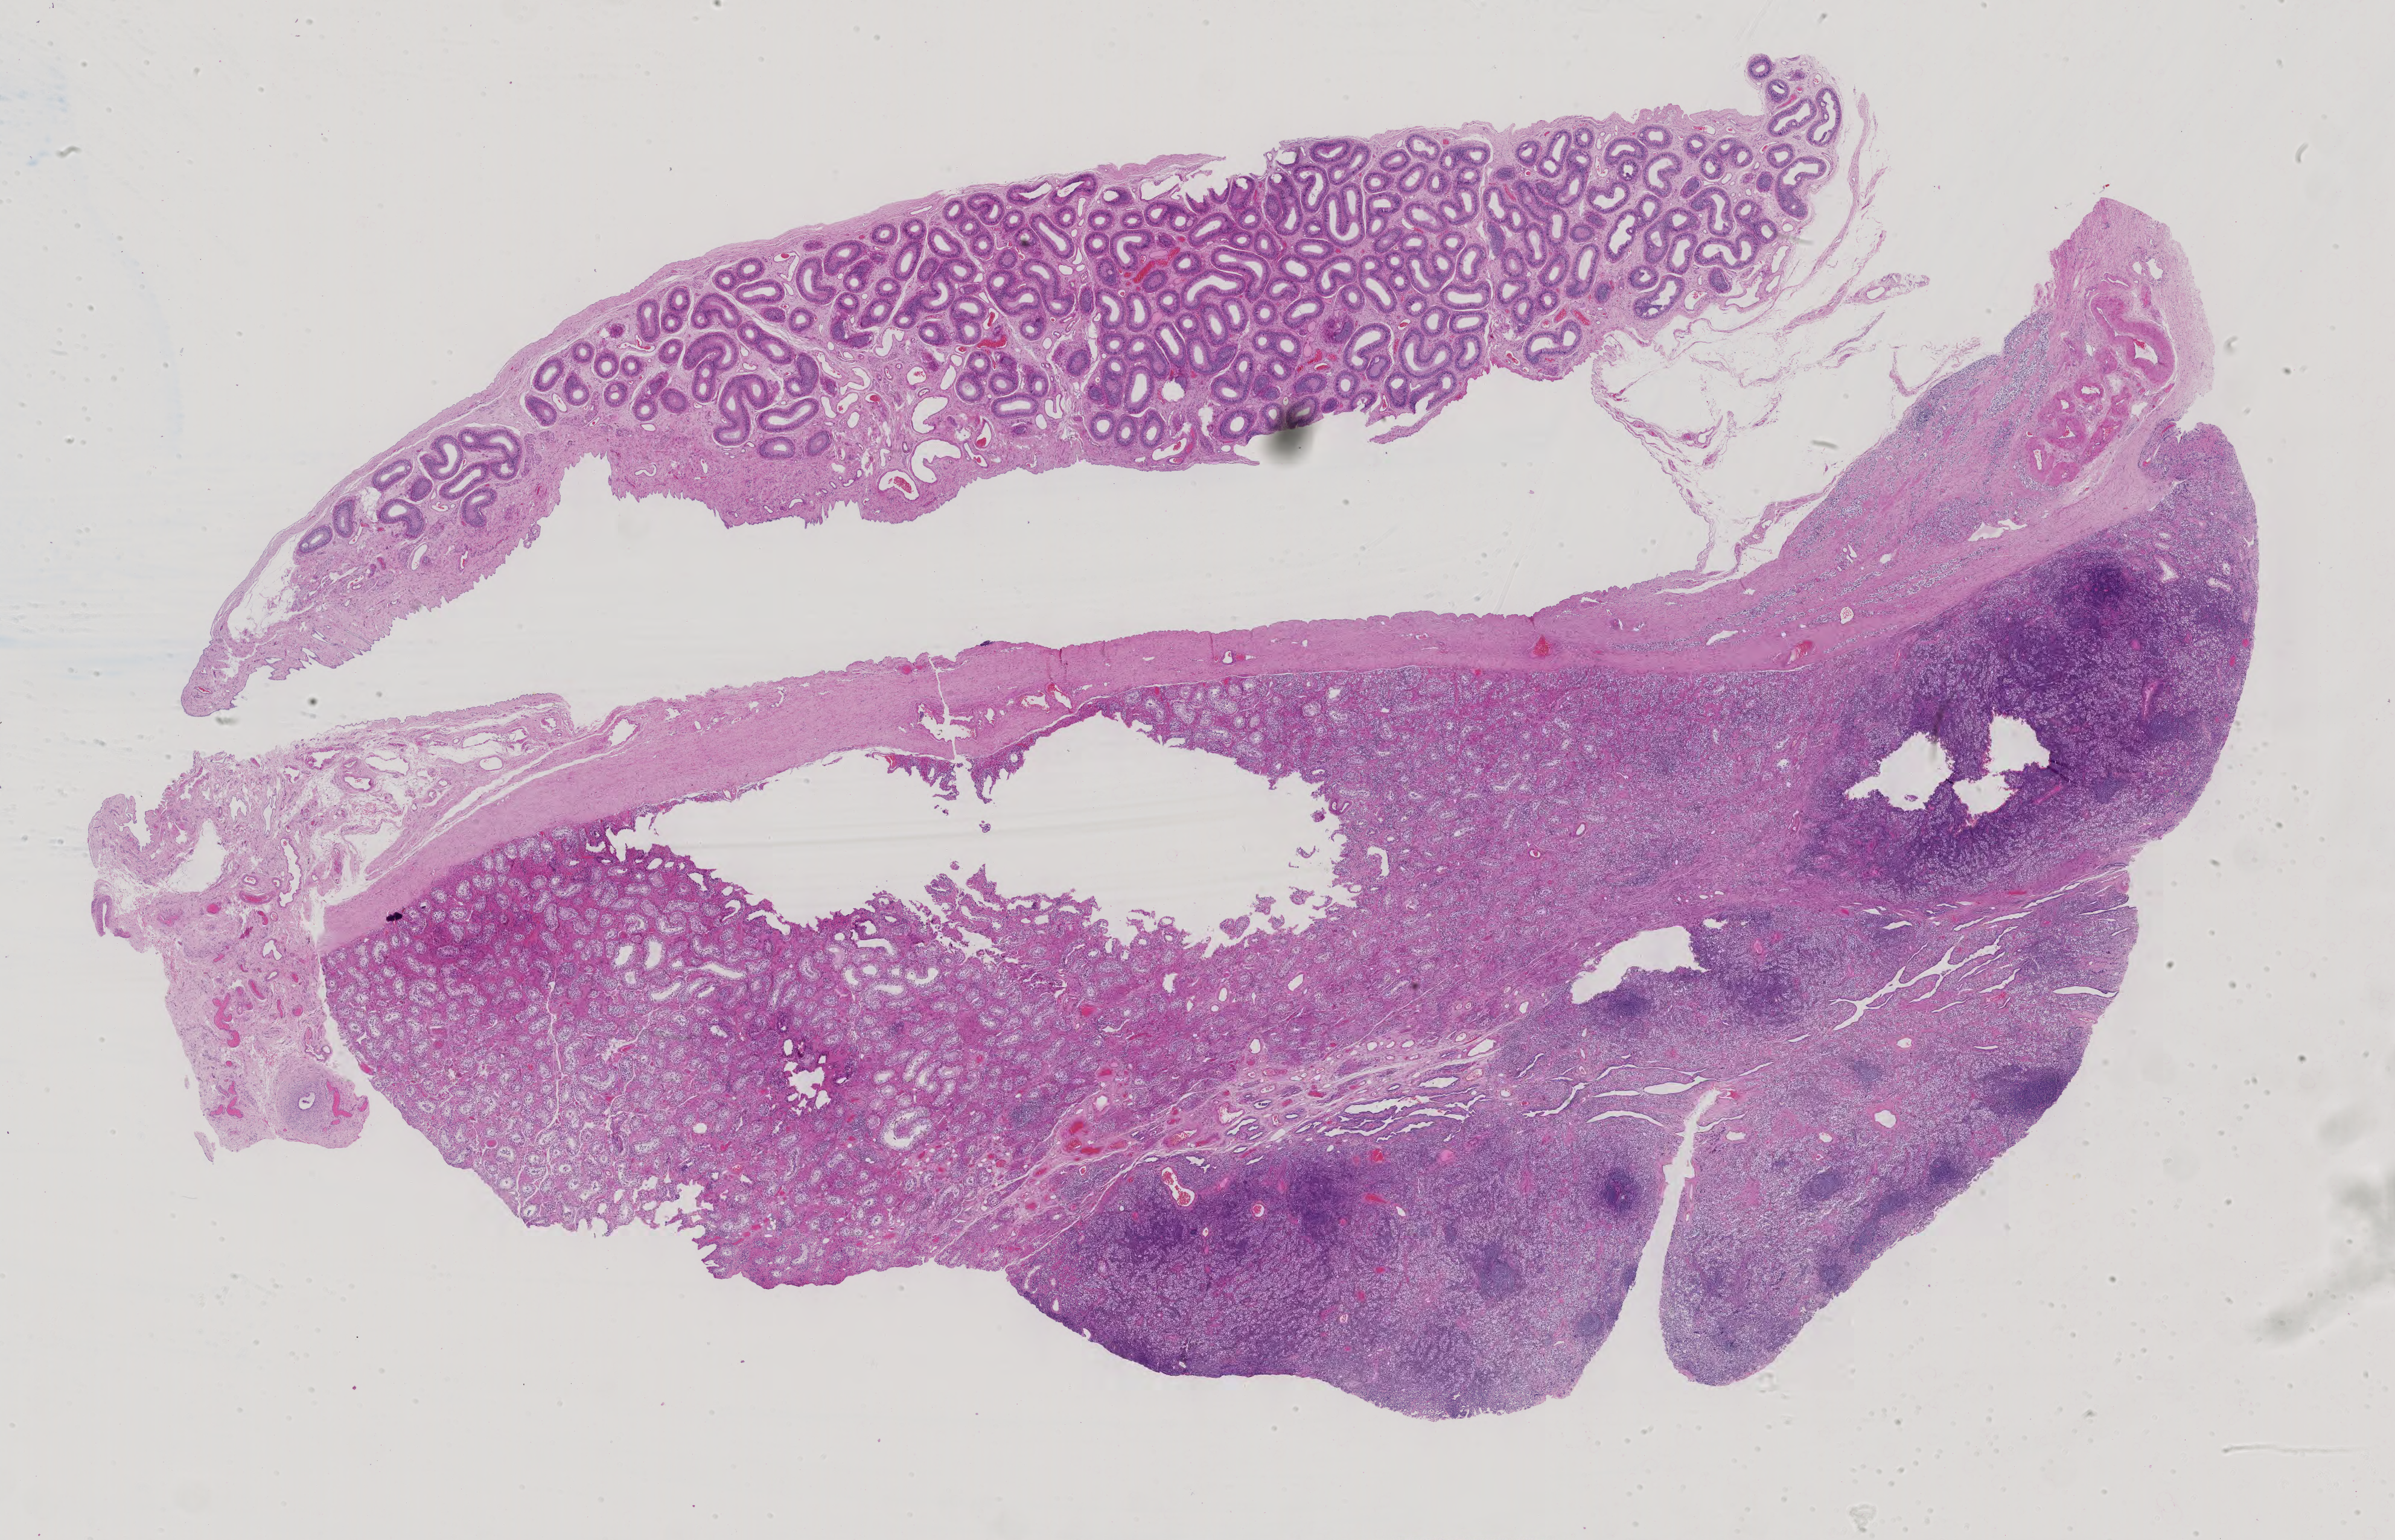
Whole-slide histology image, H&E-stained — a low-resolution overview of the entire scanned area, about 28.9 x 18.6 mm (from a 40x scan); FFPE section; additional new primary tumour sample from the testis. Patient: male, age at initial diagnosis 33 years.
This section: additional new primary tumour. Patient diagnosis: Mixed germ cell tumor.